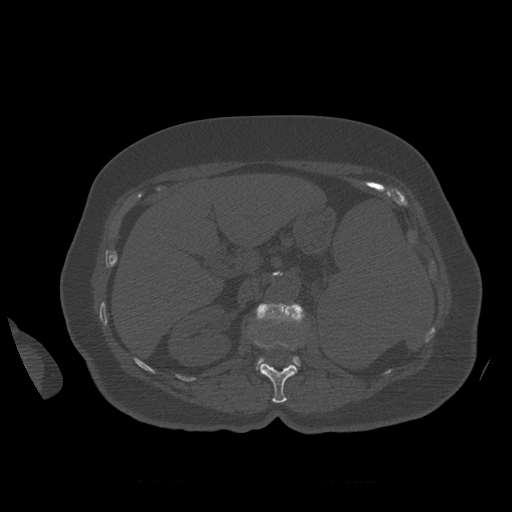
CT including the spine, one axial slice; slice 269 of 399 in the series (ordered by position); reconstruction kernel STANDARD; 120 kVp; bone window (W 1800 / L 400 HU); 1.25 mm slice thickness; 512 × 512 image matrix. Patient age 81 years. Case-level facts recorded for this patient, not image findings: primary cancer: renal; vertebrae with lytic lesions (as recorded): L1.
Annotated regions visible in this slice (semi-automatically segmented with operator editing):
- L1 vertebra: bounding box <255,341,297,404> (left, top, right, bottom; pixels)
- L2 vertebra: <256,303,305,370>